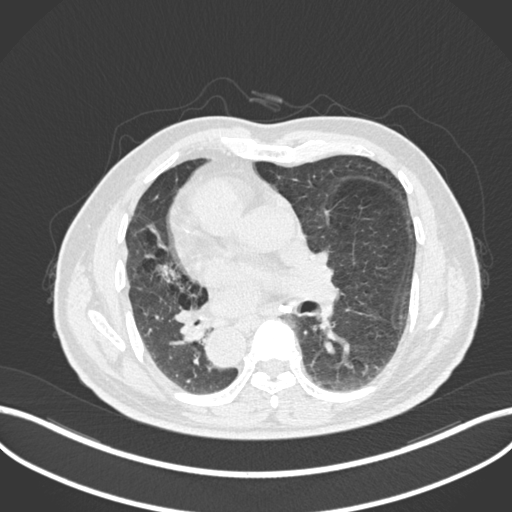
Chest CT, one axial slice; reconstruction kernel B30f; lung window (W 1500 / L -600 HU); 1 mm slice thickness; 512 × 512 image matrix, field of view 400 × 400 mm. Patient: male, 67 years. Case-level facts recorded for this patient, not image findings: clinical TNM (as recorded): T2a N0 M0.
Outlined on this slice (bounding box drawn by a radiologist):
- lung tumour (recorded histology: squamous cell carcinoma): box from (x=173, y=303) to (x=214, y=346) px